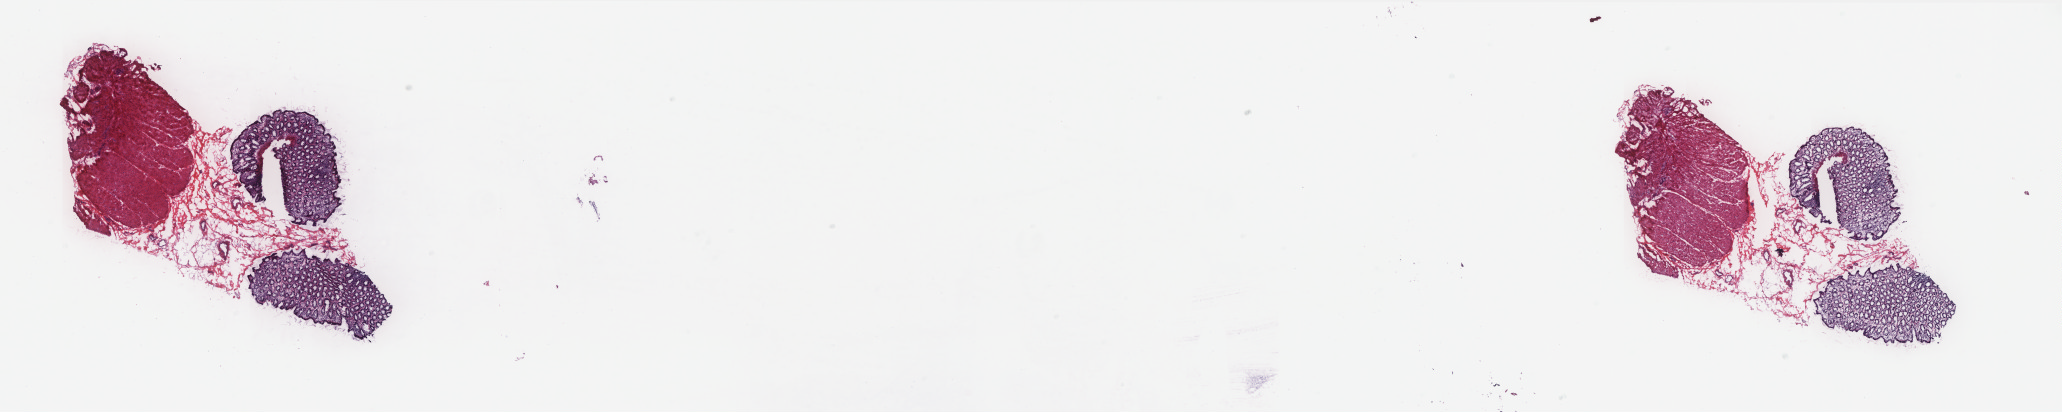
Whole-slide histology image, Hematoxylin and eosin (H&E) stained, shown as a low-resolution overview of the whole scanned area (about 32.9 x 6.6 mm), frozen section from the bottom of the tissue portion, sample: solid tissue normal (non-tumour tissue), rectum. Female patient; age at initial diagnosis 67 years. Pathologist review of this section (percent, as recorded): tumour cells 0%, normal cells 100%. Infiltration values recorded for this section: lymphocyte infiltration 30%, monocyte infiltration 7%, neutrophil infiltration 0%.
- this section: solid tissue normal (non-tumour) sample from the same patient
- patient diagnosis: Adenocarcinoma, NOS